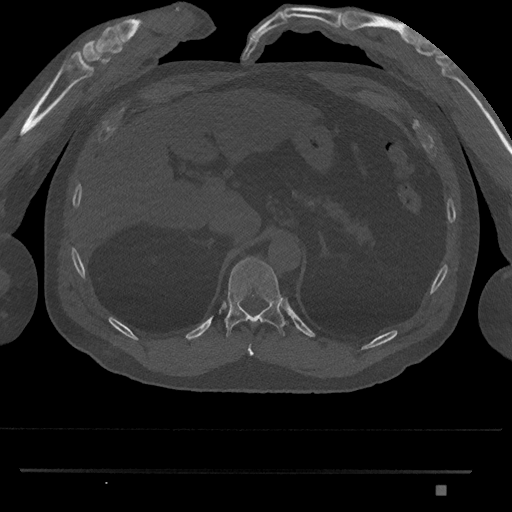
CT including the spine, one axial slice. Slice 952 of 1134 in the series (ordered by position). Bone window (W 1800 / L 400 HU). 512 × 512 image matrix. Patient: male, 65 years. Case-level facts recorded for this patient, not image findings: primary cancer: prostate.
Outlined on this slice (semi-automatic segmentation, software-assisted and operator-edited):
- T10 vertebra: box from (x=247, y=344) to (x=254, y=356) px
- T11 vertebra: (x=225, y=257)–(x=289, y=337)